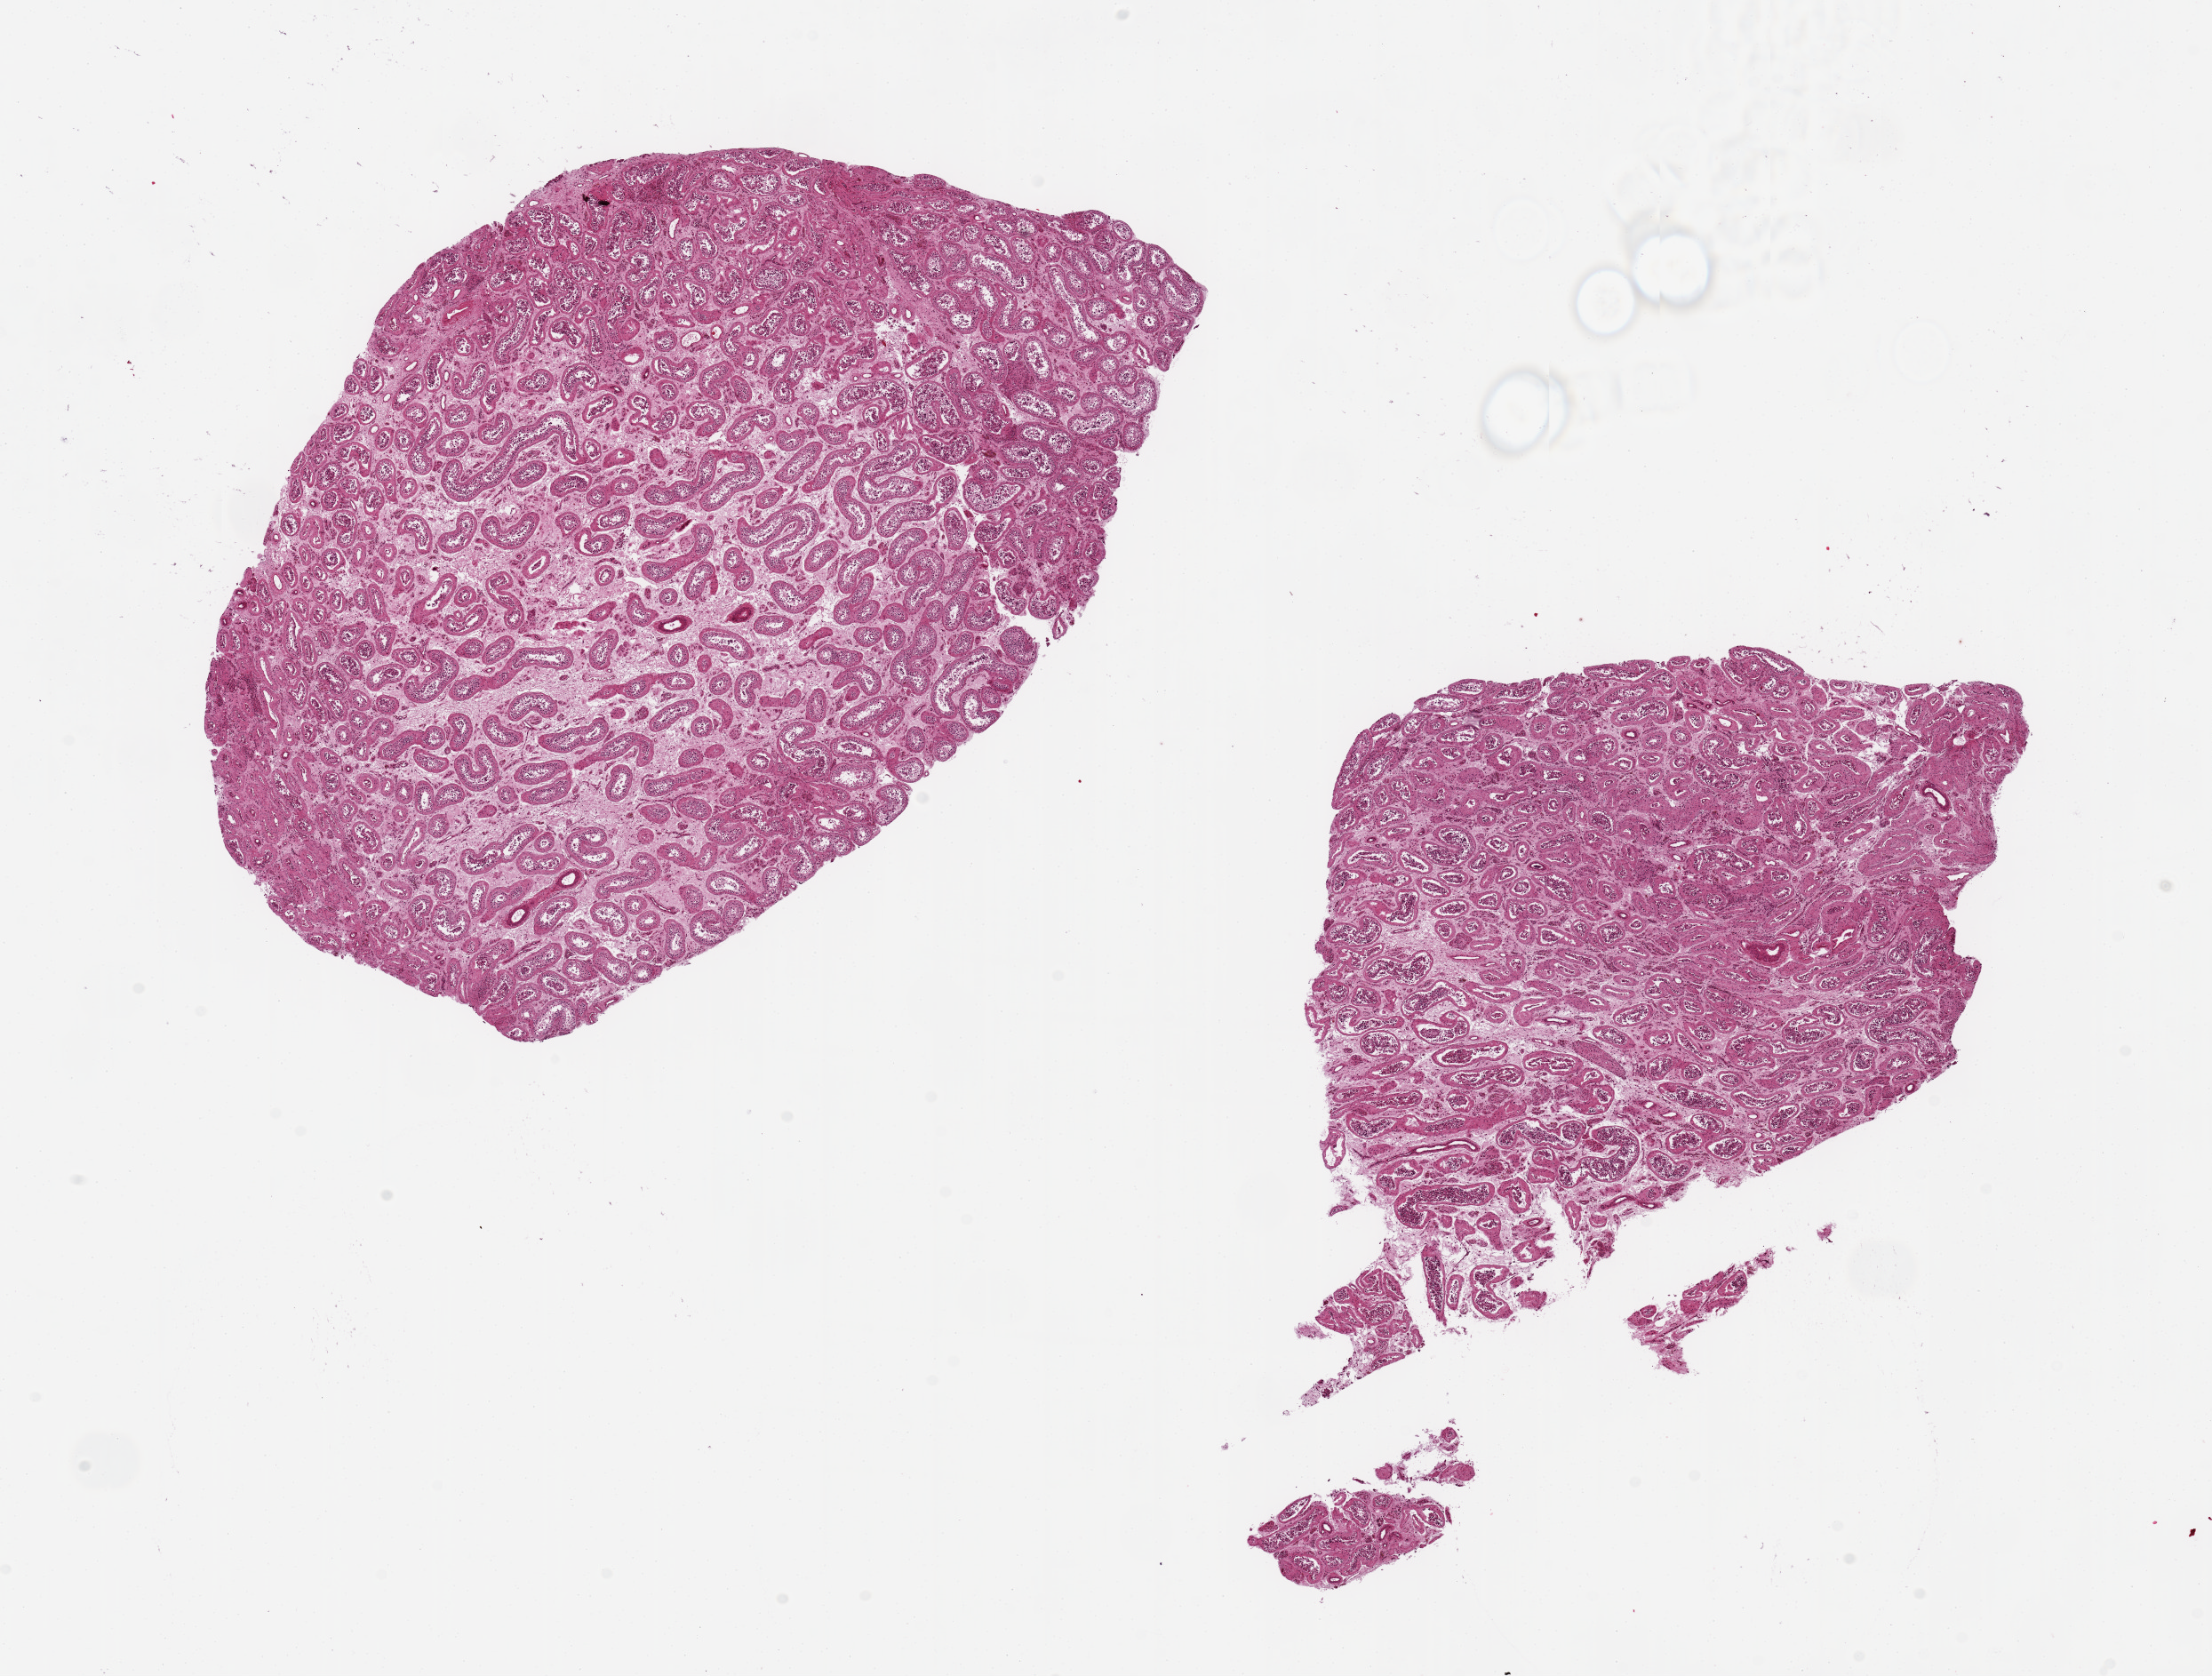
Whole-slide image, H&E stain, whole scanned area (about 19.7 x 14.9 mm, from a 20x scan) shown as a low-resolution overview; PAXgene-fixed paraffin-embedded (PFPE) section; sampled site (target tissue): testis; donor tissue sample.
Pathologist's review note for this sample: 2 aliquots. Spermatogenesis present.